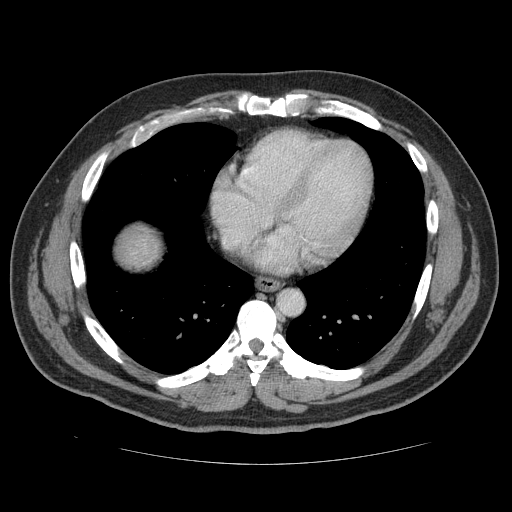
Contrast-enhanced abdominal CT (liver protocol), one axial slice. Slice 112 of 113 in the series (ordered by position). Reconstruction kernel STANDARD. Soft-tissue window (W 400 / L 40 HU). 2.5 mm slice thickness. 512 × 512 image matrix, field of view 400 × 400 mm. From the clinical record (not read from this slice): diagnosis: hepatocellular carcinoma (patient treated with transarterial chemoembolisation; whether this scan precedes or follows treatment is not stated here); TNM stage (as recorded): Stage-II; Child-Pugh class: B; tumour differentiation: moderately differentiated; tumour size: 4.8 cm.
Structures marked on this image (semi-automatic segmentation, software-assisted and operator-edited):
- liver parenchyma outside the tumour (the mass and vessels are separate outlines, so this box may not span the whole liver): bounding box (x1, y1, x2, y2) in pixels: (124, 234, 146, 252)